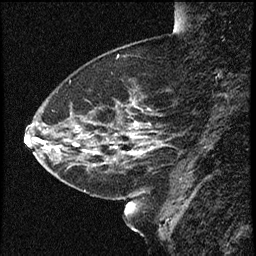
Breast MRI (dynamic contrast-enhanced), one sagittal slice; dynamic contrast-enhanced study with each time point stored as its own series, time point 2 of 4 at this slice position (early post-contrast, ordered by acquisition time); 1.5 T; TE 4.2 ms, TR 16.7 ms; 2 mm slice thickness; 256 × 256 image matrix, field of view 200 × 200 mm. Patient: female, 52 years. From the clinical record (not read from this slice): setting: breast cancer imaged before/during neoadjuvant chemotherapy; receptor status: HER2-positive.
Structures marked on this image (semi-automatic segmentation, software-assisted and operator-edited):
- analysis volume of interest (the breast-tissue region the enhancement analysis was run in; not a lesion): bounding box (x1, y1, x2, y2) in pixels: (37, 79, 159, 181)
- tumour enhancement mask (voxels above the 100 % enhancement threshold inside the analysis volume of interest): (113, 107, 139, 142)